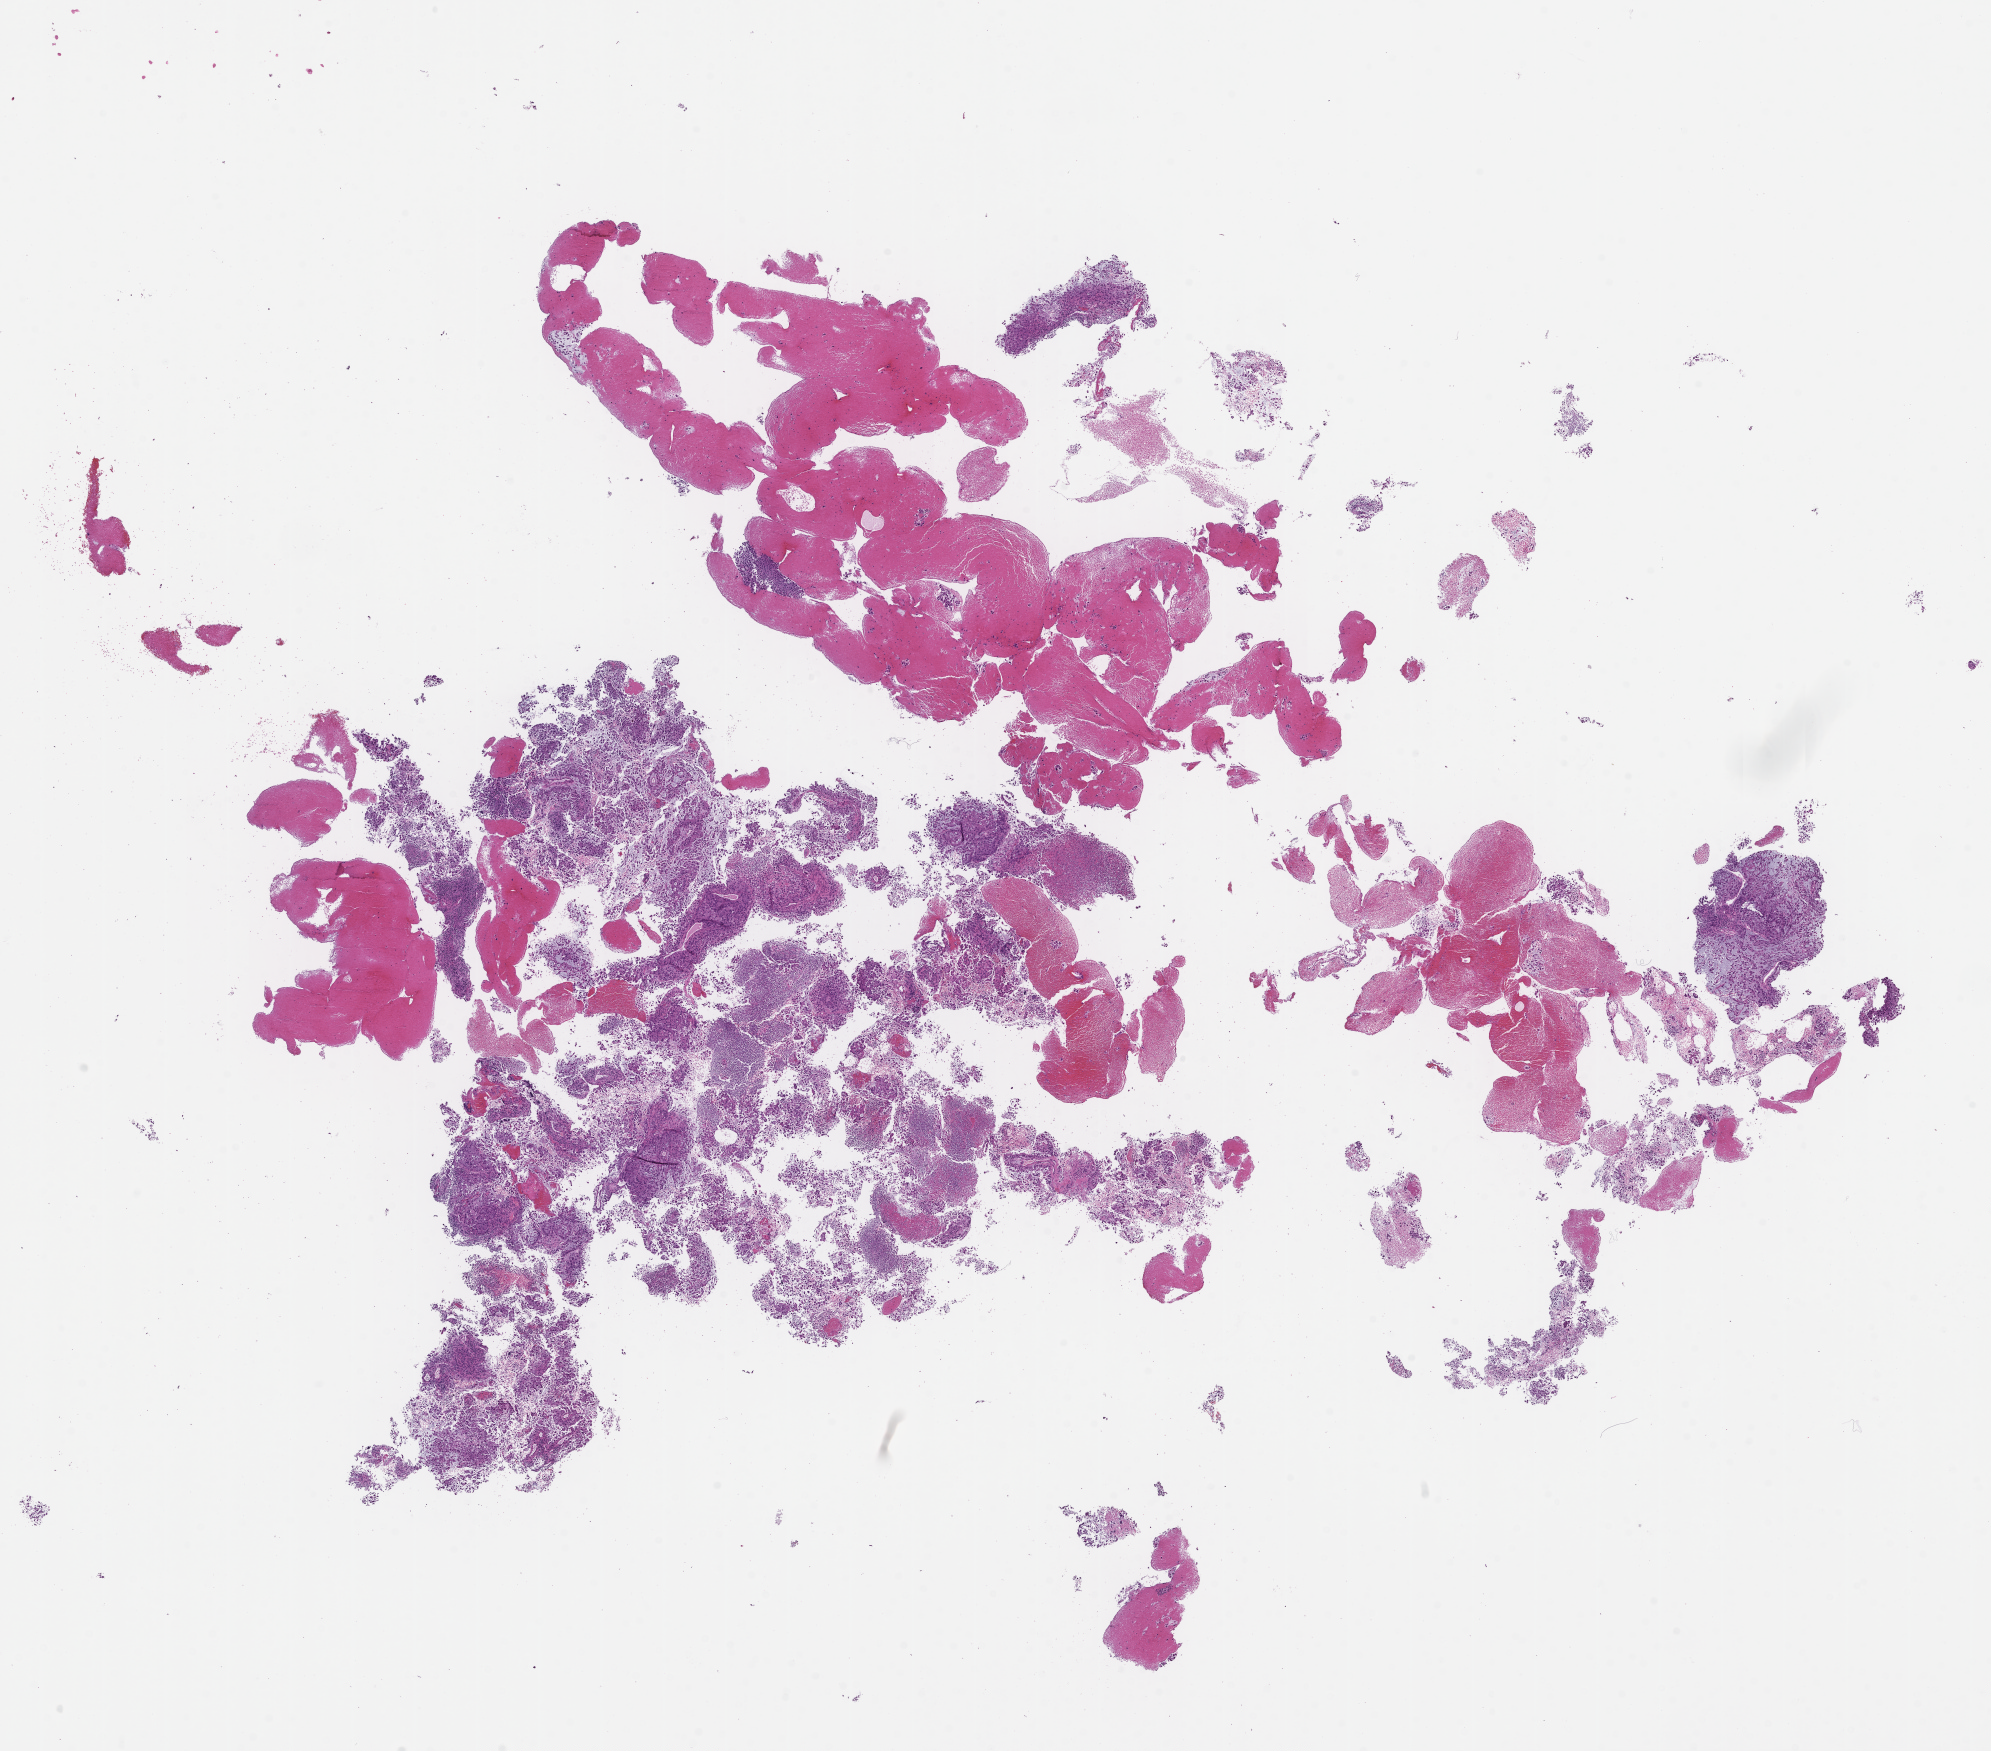
Whole-slide image, haematoxylin and eosin stain — low-resolution overview of the scanned area, about 16.1 x 14.1 mm. Formalin-fixed, paraffin-embedded (FFPE) tissue. Site: lung. Patient: male.
This section: primary tumor. Diagnosis: Non-Small Cell Lung Carcinoma.